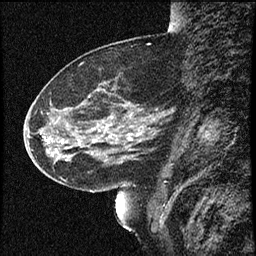
Breast MRI (dynamic contrast-enhanced), one sagittal slice; position 25 of 60 along the scan axis; dynamic contrast-enhanced study with each time point stored as its own series, time point 2 of 4 at this slice position (early post-contrast, ordered by acquisition time); 1.5 T; TE 4.2 ms, TR 16.7 ms; 2 mm slice thickness; 256 × 256 image matrix. Patient: female, 52 years. From the clinical record (not read from this slice): setting: breast cancer imaged before/during neoadjuvant chemotherapy; receptor status: HER2-positive.
Outlined on this slice (semi-automatically segmented with operator editing):
- analysis volume of interest (the breast-tissue region the enhancement analysis was run in; not a lesion): bounding box (x1, y1, x2, y2) in pixels: (37, 79, 165, 181)
- tumour enhancement mask (voxels above the 100 % enhancement threshold inside the analysis volume of interest): (128, 134, 138, 135)